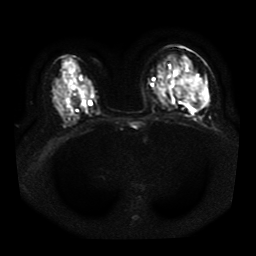
Breast MRI, one axial slice. Position 20 of 41 along the scan axis. Diffusion-weighted series; image 2 of 4 stored at this slice position (different b-values; order by instance number). 1.5 T. 256 × 256 image matrix, field of view 330 × 330 mm. Female patient.
Outlined on this slice (outlined manually by an expert reader):
- tumour on diffusion-weighted imaging: bounding box [x1, y1, x2, y2] px = [174, 74, 206, 108]